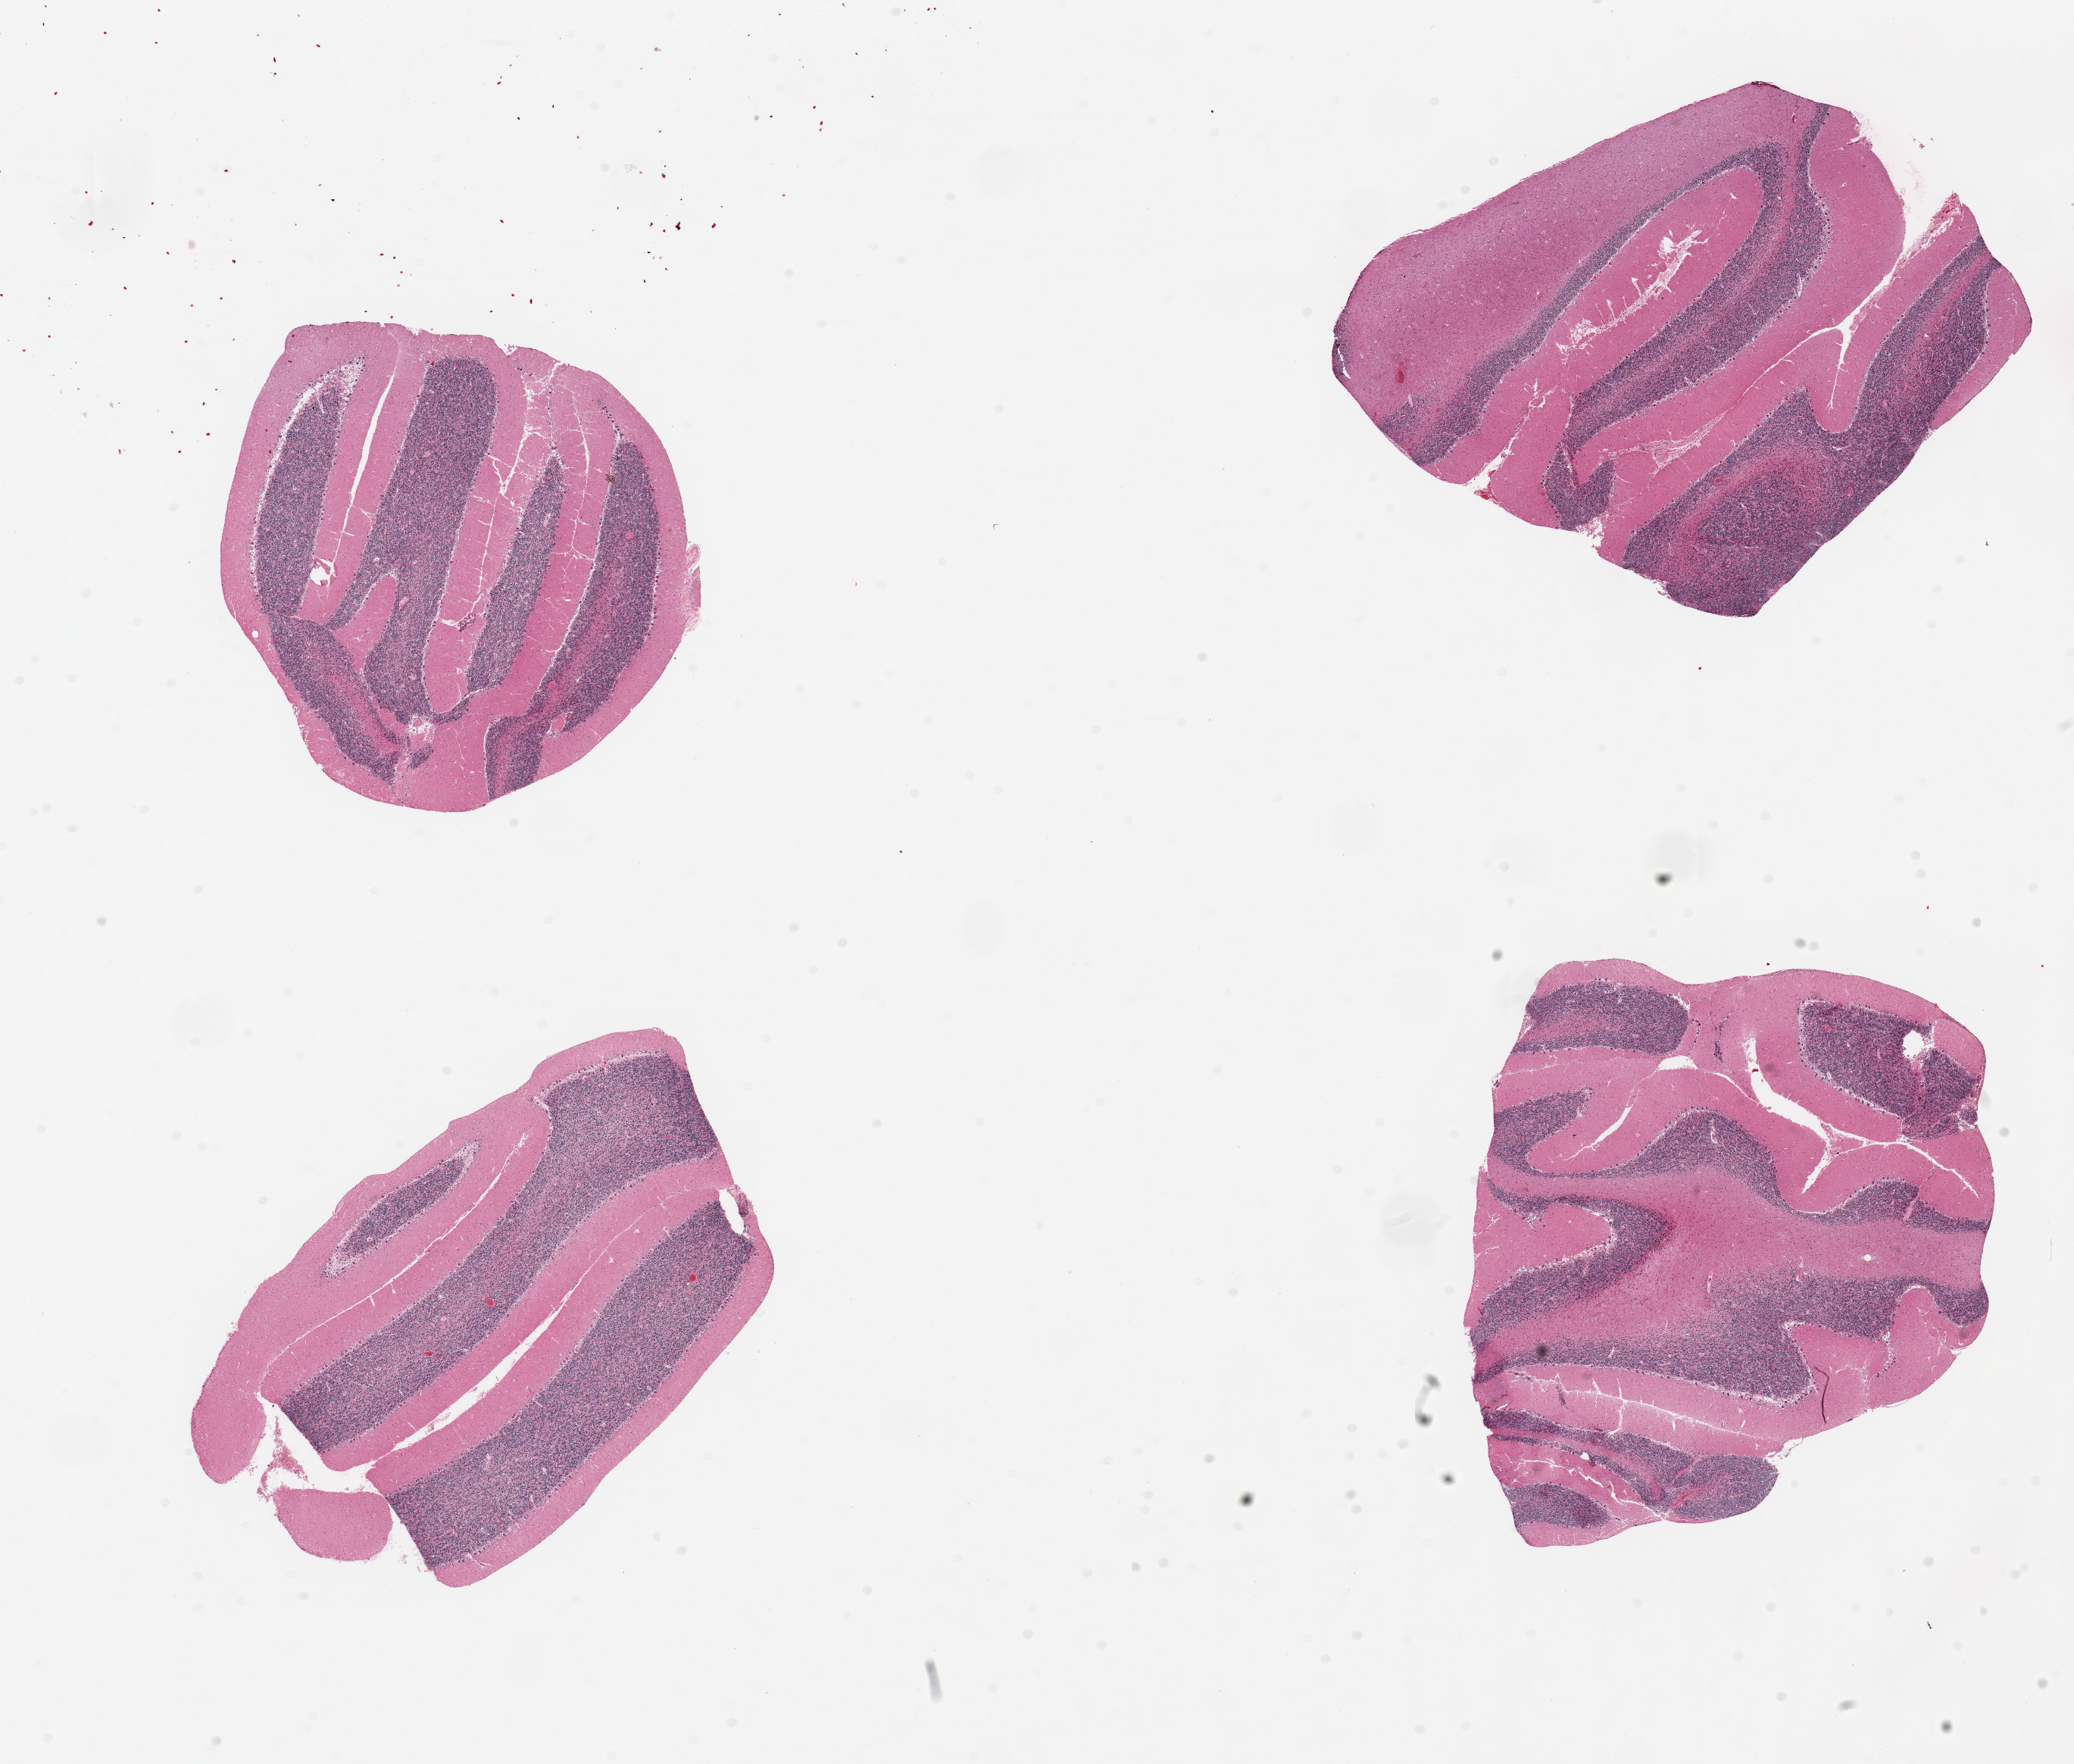
Whole-slide image, H&E stain, whole scanned area (about 21.7 x 18.4 mm, from a 20x scan) shown as a low-resolution overview; PAXgene-fixed, paraffin-embedded tissue; target tissue: cerebellum; donor tissue sample. Donor: male.
* review note (as recorded): 4 pieces